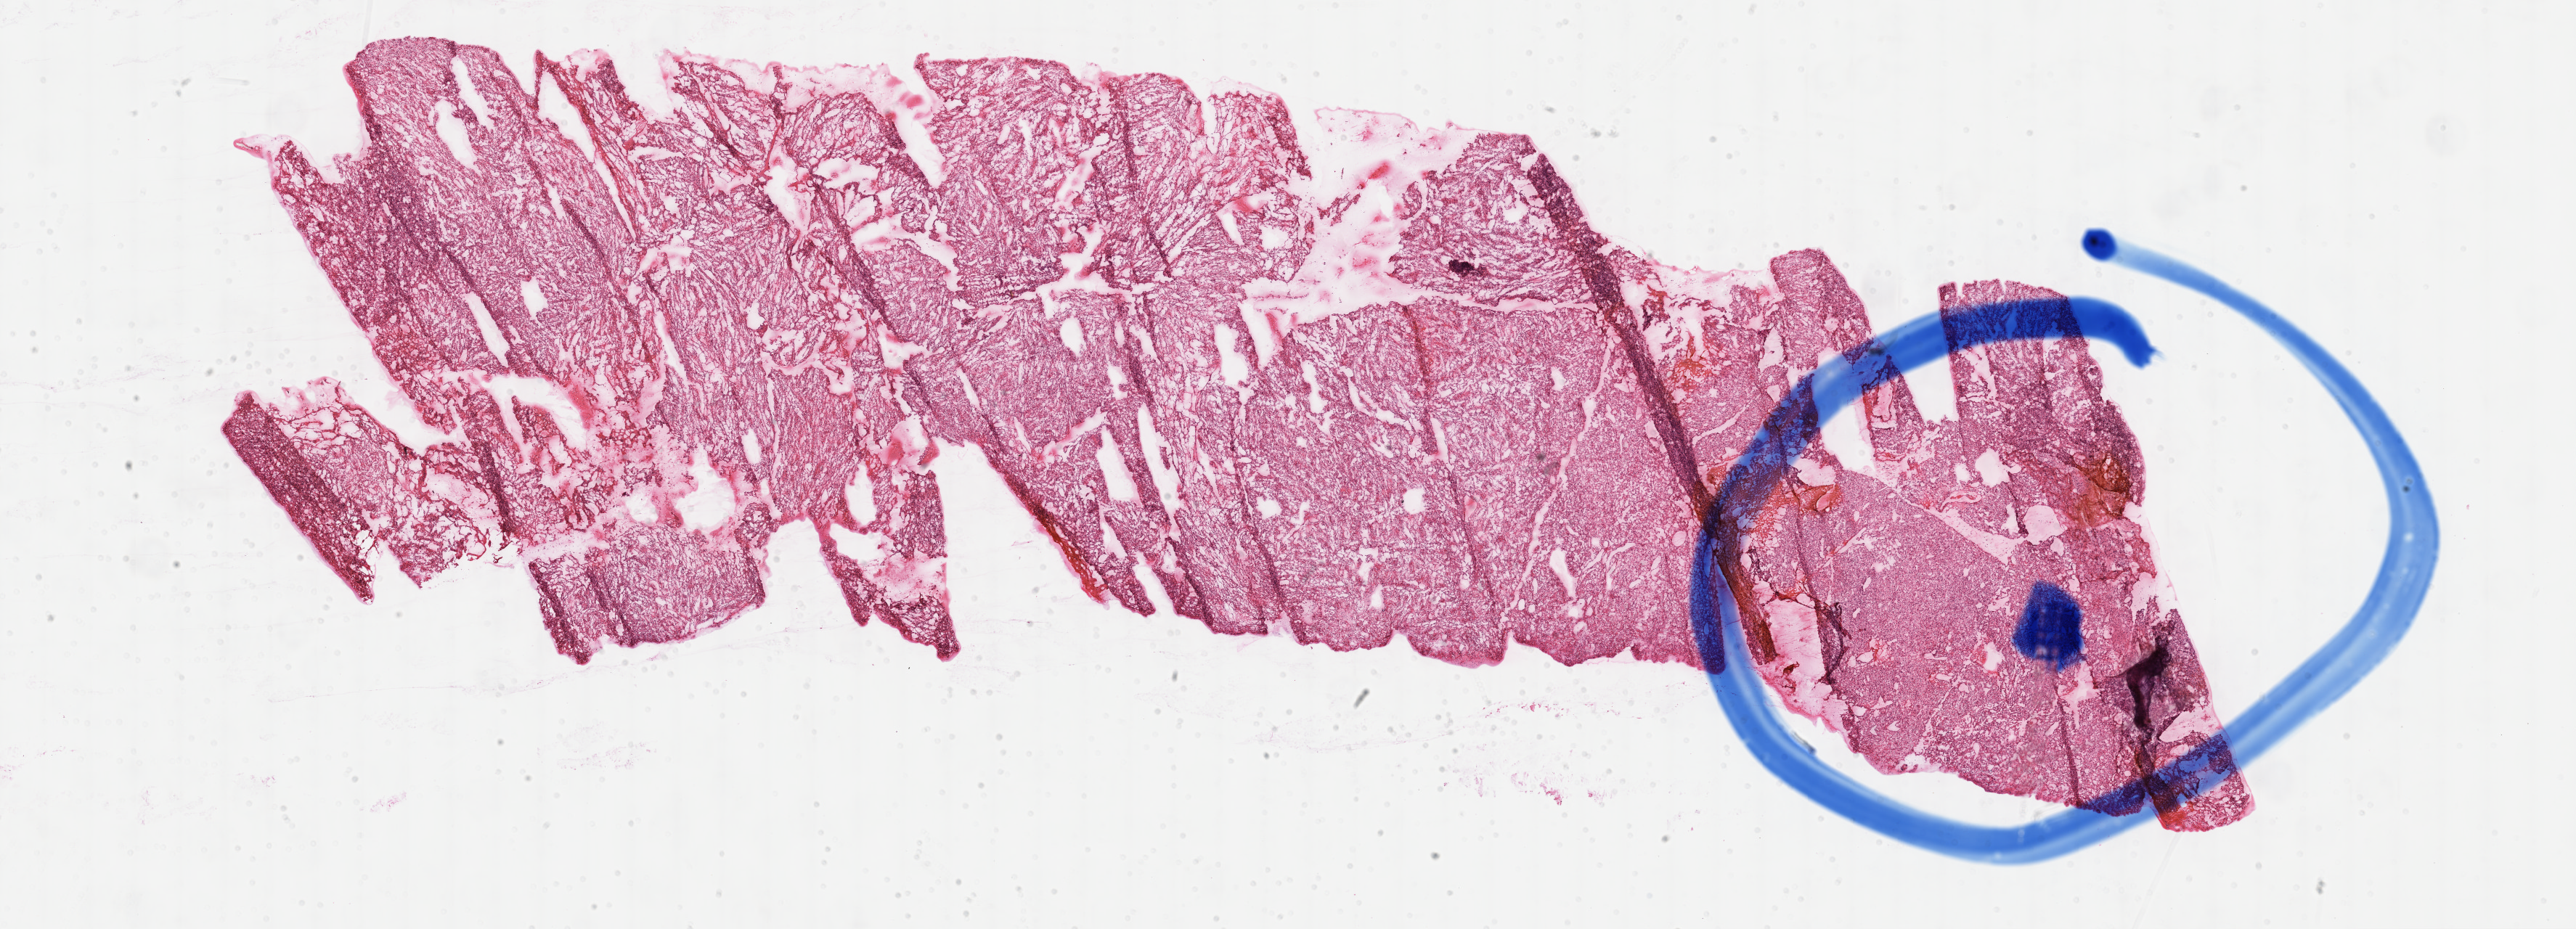
Digitized Hematoxylin and eosin (H&E) stained tissue section (whole slide), shown as a low-resolution overview of the whole scanned area (about 28.7 x 10.4 mm, slide scanned at 40x), formalin-fixed paraffin-embedded (FFPE) diagnostic section, primary tumour sample from the kidney. Patient: male, age at initial diagnosis 78 years. Histologic grade: G3 (poorly differentiated).
Histologic diagnosis: Clear cell adenocarcinoma, NOS. AJCC pathologic stage: I. TNM: T1b NX M0.